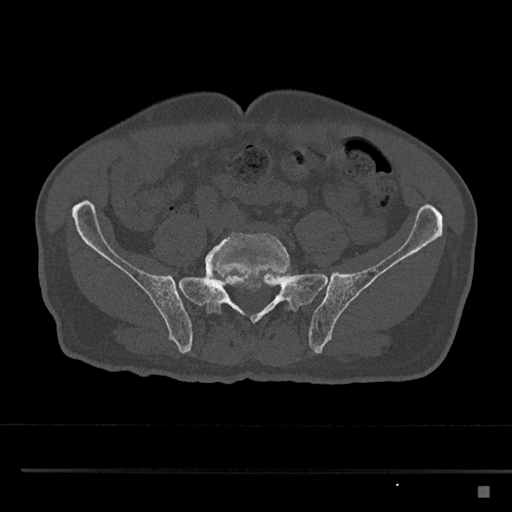
CT including the spine, one axial slice. Slice 554 of 797 in the series (ordered by position). Bone window (W 1800 / L 400 HU). 0.5 mm slice thickness. 512 × 512 image matrix. Patient: male, 59 years. Case-level facts recorded for this patient, not image findings: primary cancer: prostate.
Structures marked on this image (semi-automatic segmentation, software-assisted and operator-edited):
- L5 vertebra: box from (x=205, y=232) to (x=291, y=314) px